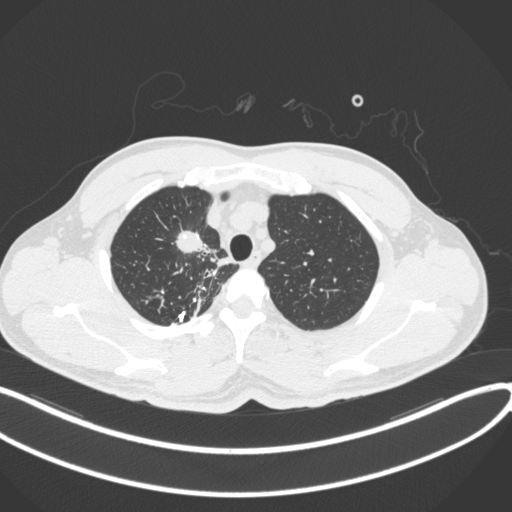
Chest CT, one axial slice; slice 310 of 391 in the series (ordered by position); reconstruction kernel B31f; 120 kVp; lung window (W 1500 / L -600 HU); 1 mm slice thickness; 512 × 512 image matrix, field of view 400 × 400 mm. Male patient, age 48 years. From the clinical record (not read from this slice): clinical TNM (as recorded): T1c N1 M1.
Annotated regions visible in this slice (rectangle marked by the reading radiologist):
- lung tumour (recorded histology: adenocarcinoma): bounding box (x1, y1, x2, y2) in pixels: (170, 226, 210, 263)